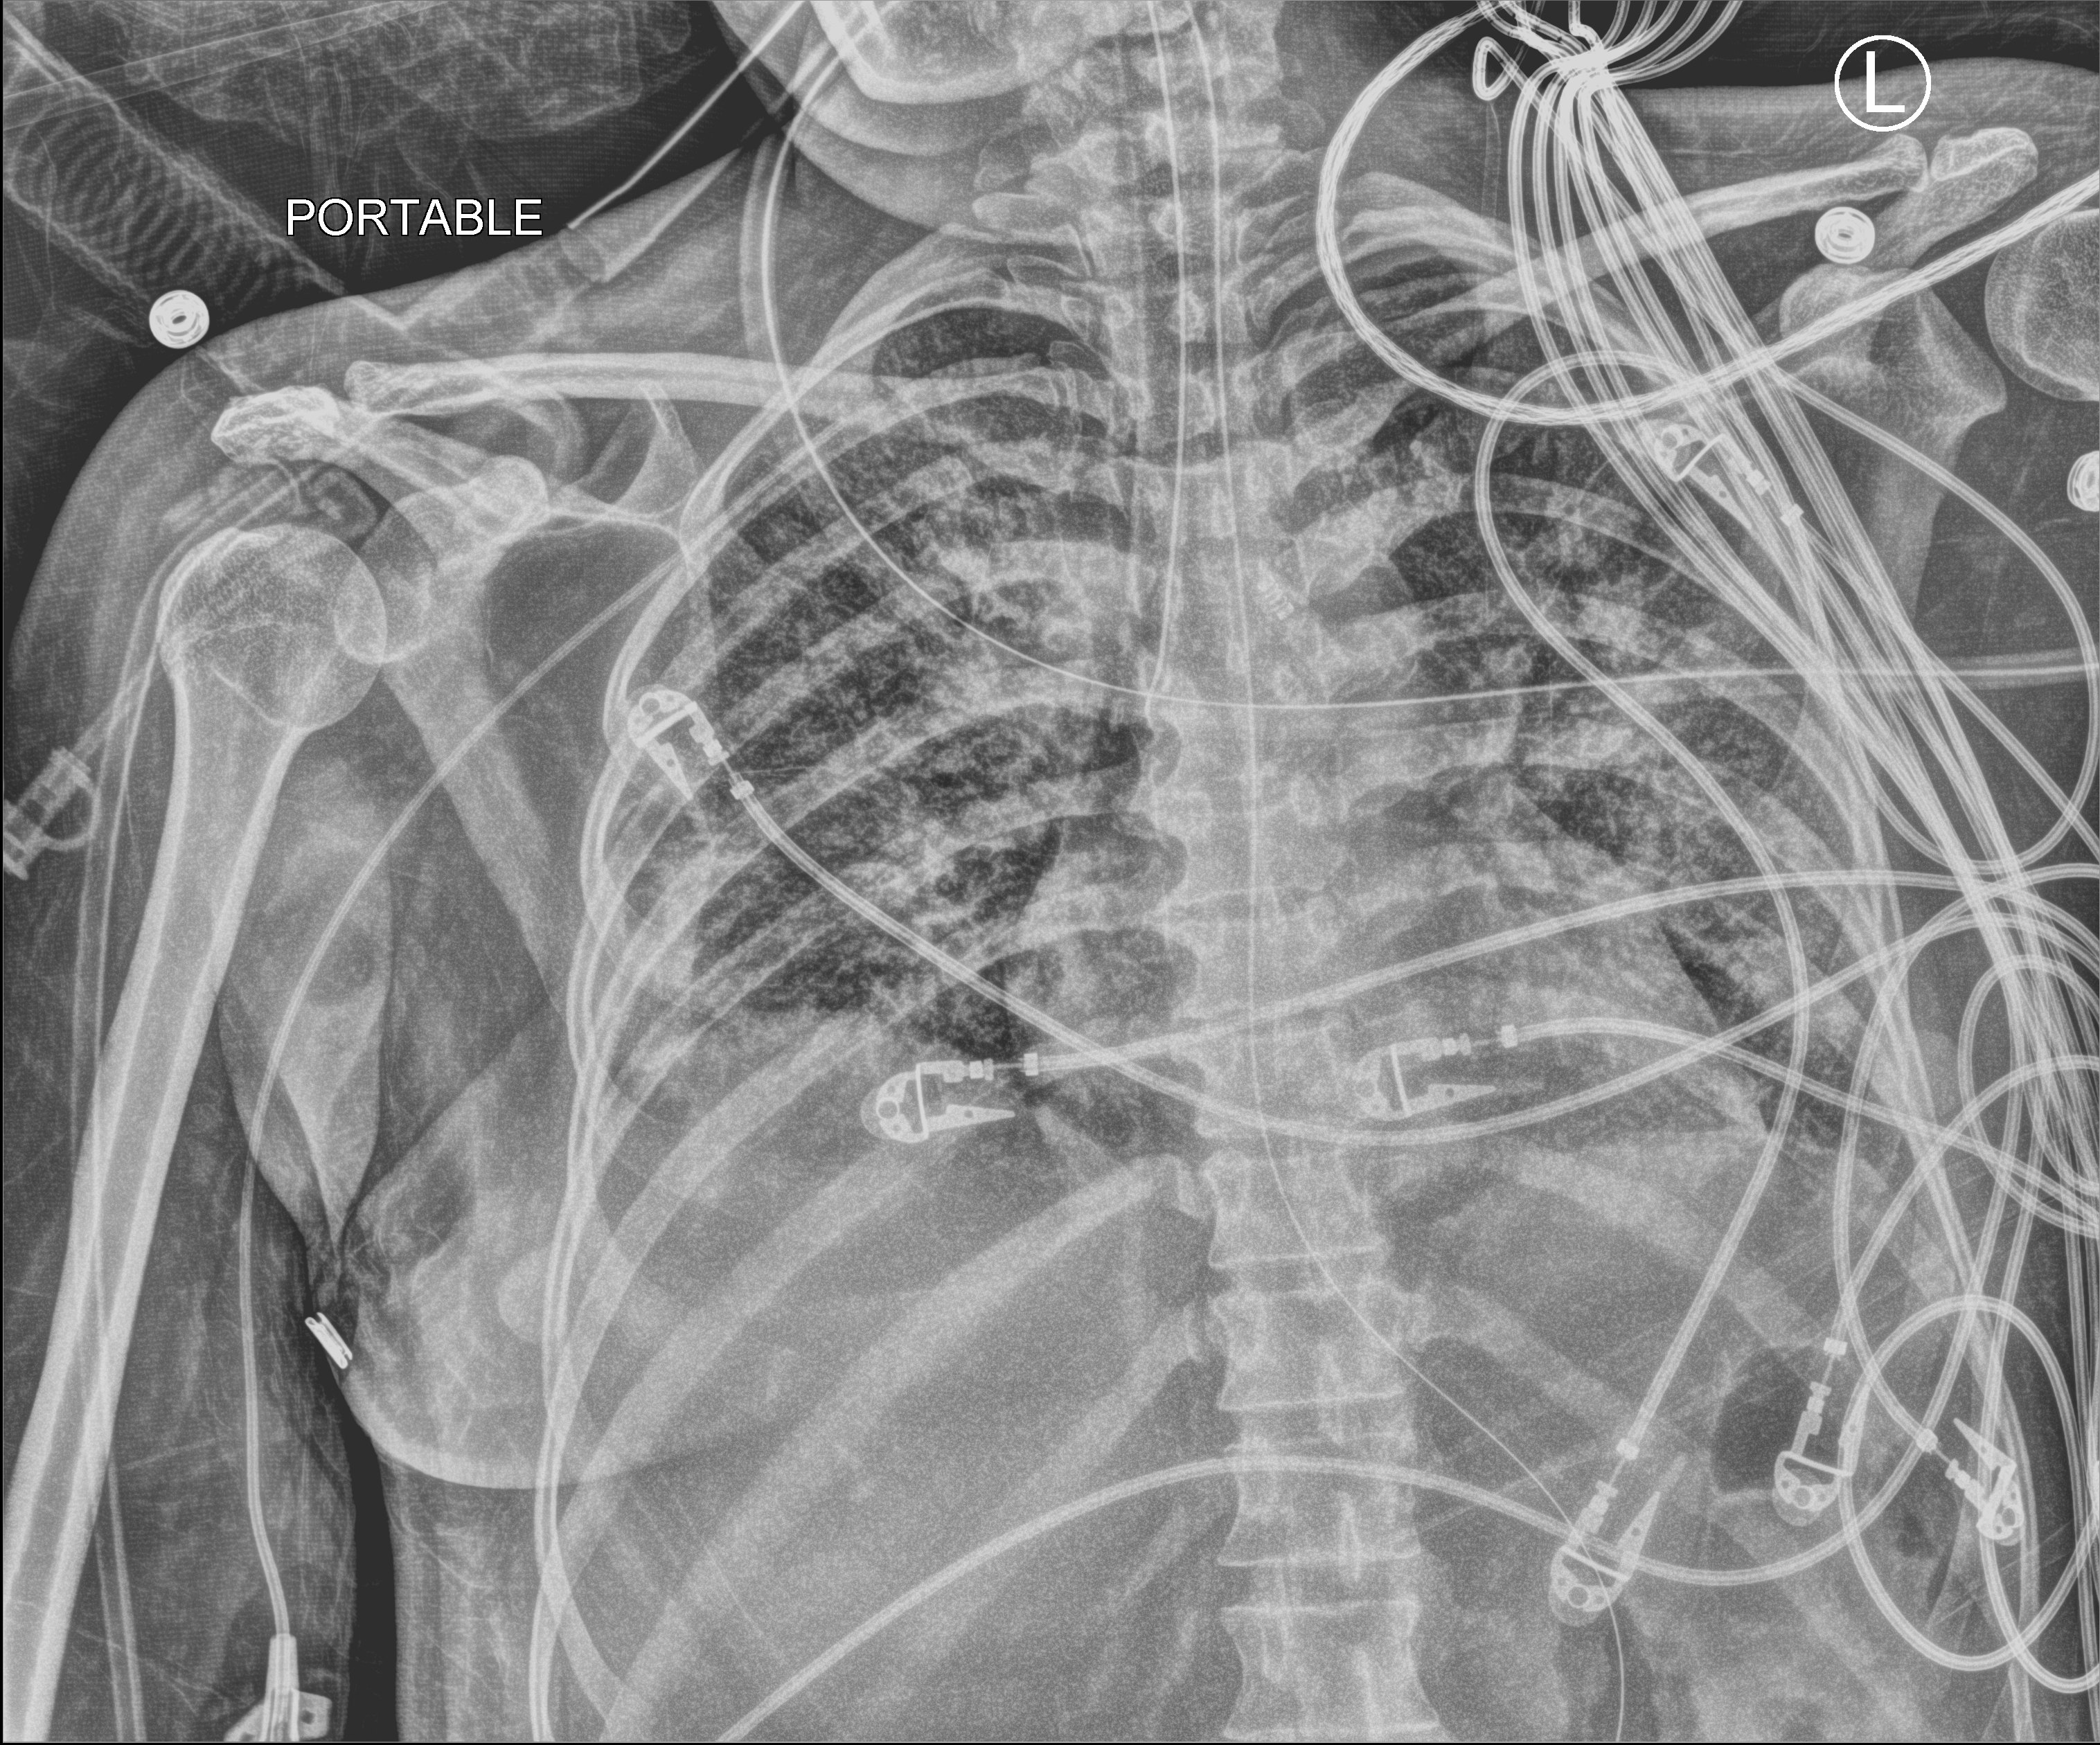
Bedside chest radiograph (computed radiography). Female patient hospitalised with COVID-19, age 18–59 years.
Hospital-stay facts (about this admission, not read from this image; timing relative to this image not recorded): length of hospital stay: 71 days; admitted to intensive care during this hospital stay: yes; mechanically ventilated during this hospital stay: yes.